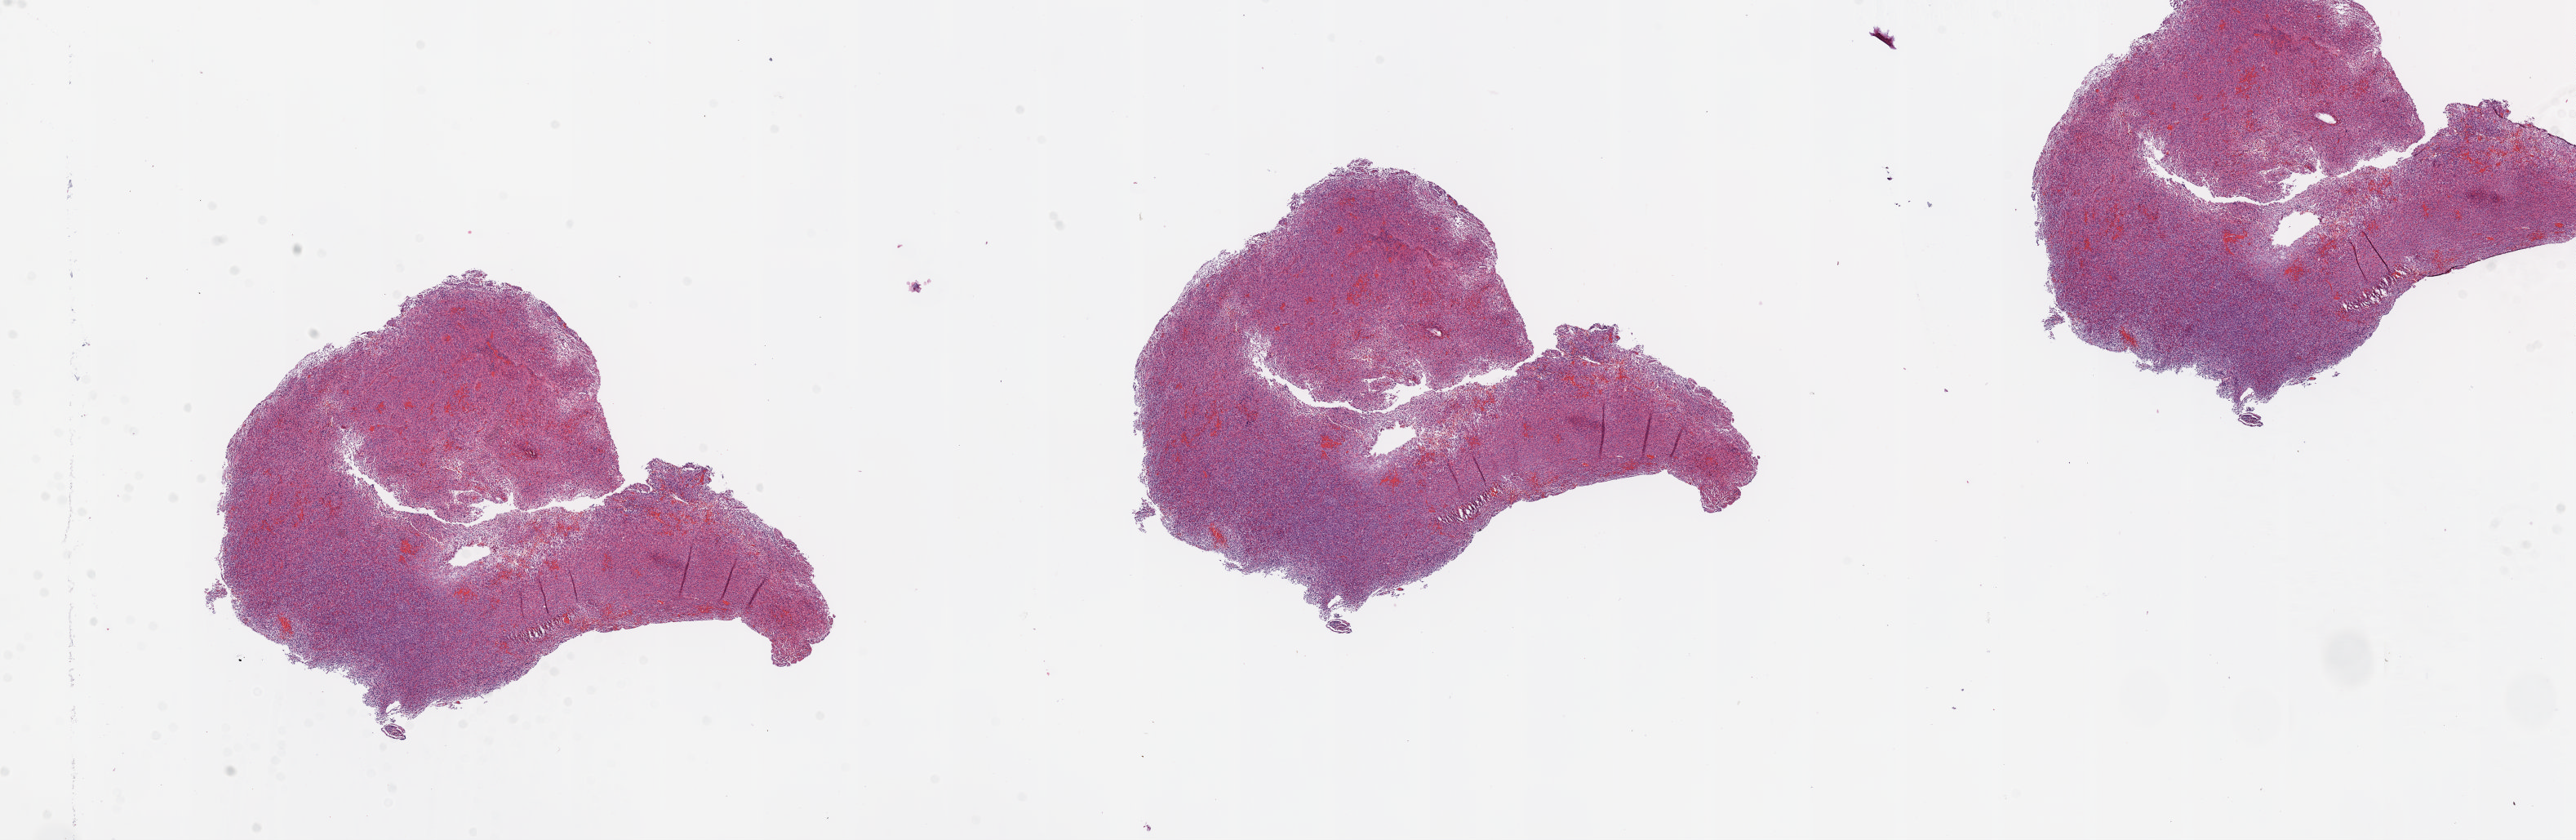
Digitized Hematoxylin and eosin (H&E) stained tissue section (whole slide), low-resolution overview of the scanned area, about 25.3 x 8.2 mm. Frozen section. Sample: primary tumour, brain. Patient: male, age at initial diagnosis 67 years. Composition of this section per pathologist review: tumour cells 100%, tumour nuclei 85%, normal cells 0%, stromal cells 0%, necrosis 0%.
Pathologic diagnosis: Glioblastoma.